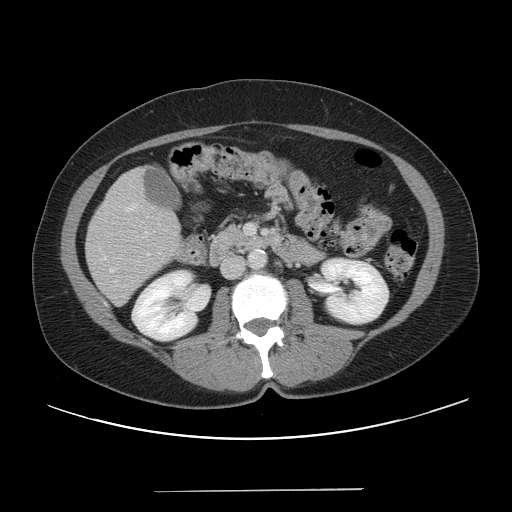
Contrast-enhanced abdominal CT, one axial slice; position 16 of 56 along the scan axis; 120 kVp; soft-tissue window (W 400 / L 40 HU); 5 mm slice thickness; 512 × 512 image matrix, field of view 419 × 419 mm. Female patient, age 54 years. Case-level facts recorded for this patient, not image findings: diagnosis: colorectal cancer liver metastases, imaged before liver resection; multiple liver metastases: yes; largest metastasis: 3.2 cm; disease in both lobes: yes.
Annotated regions visible in this slice (manually delineated by an expert):
- liver: bounding box <87,169,182,304> (left, top, right, bottom; pixels)
- portal vein (with intrahepatic branches): <247,225,254,233>